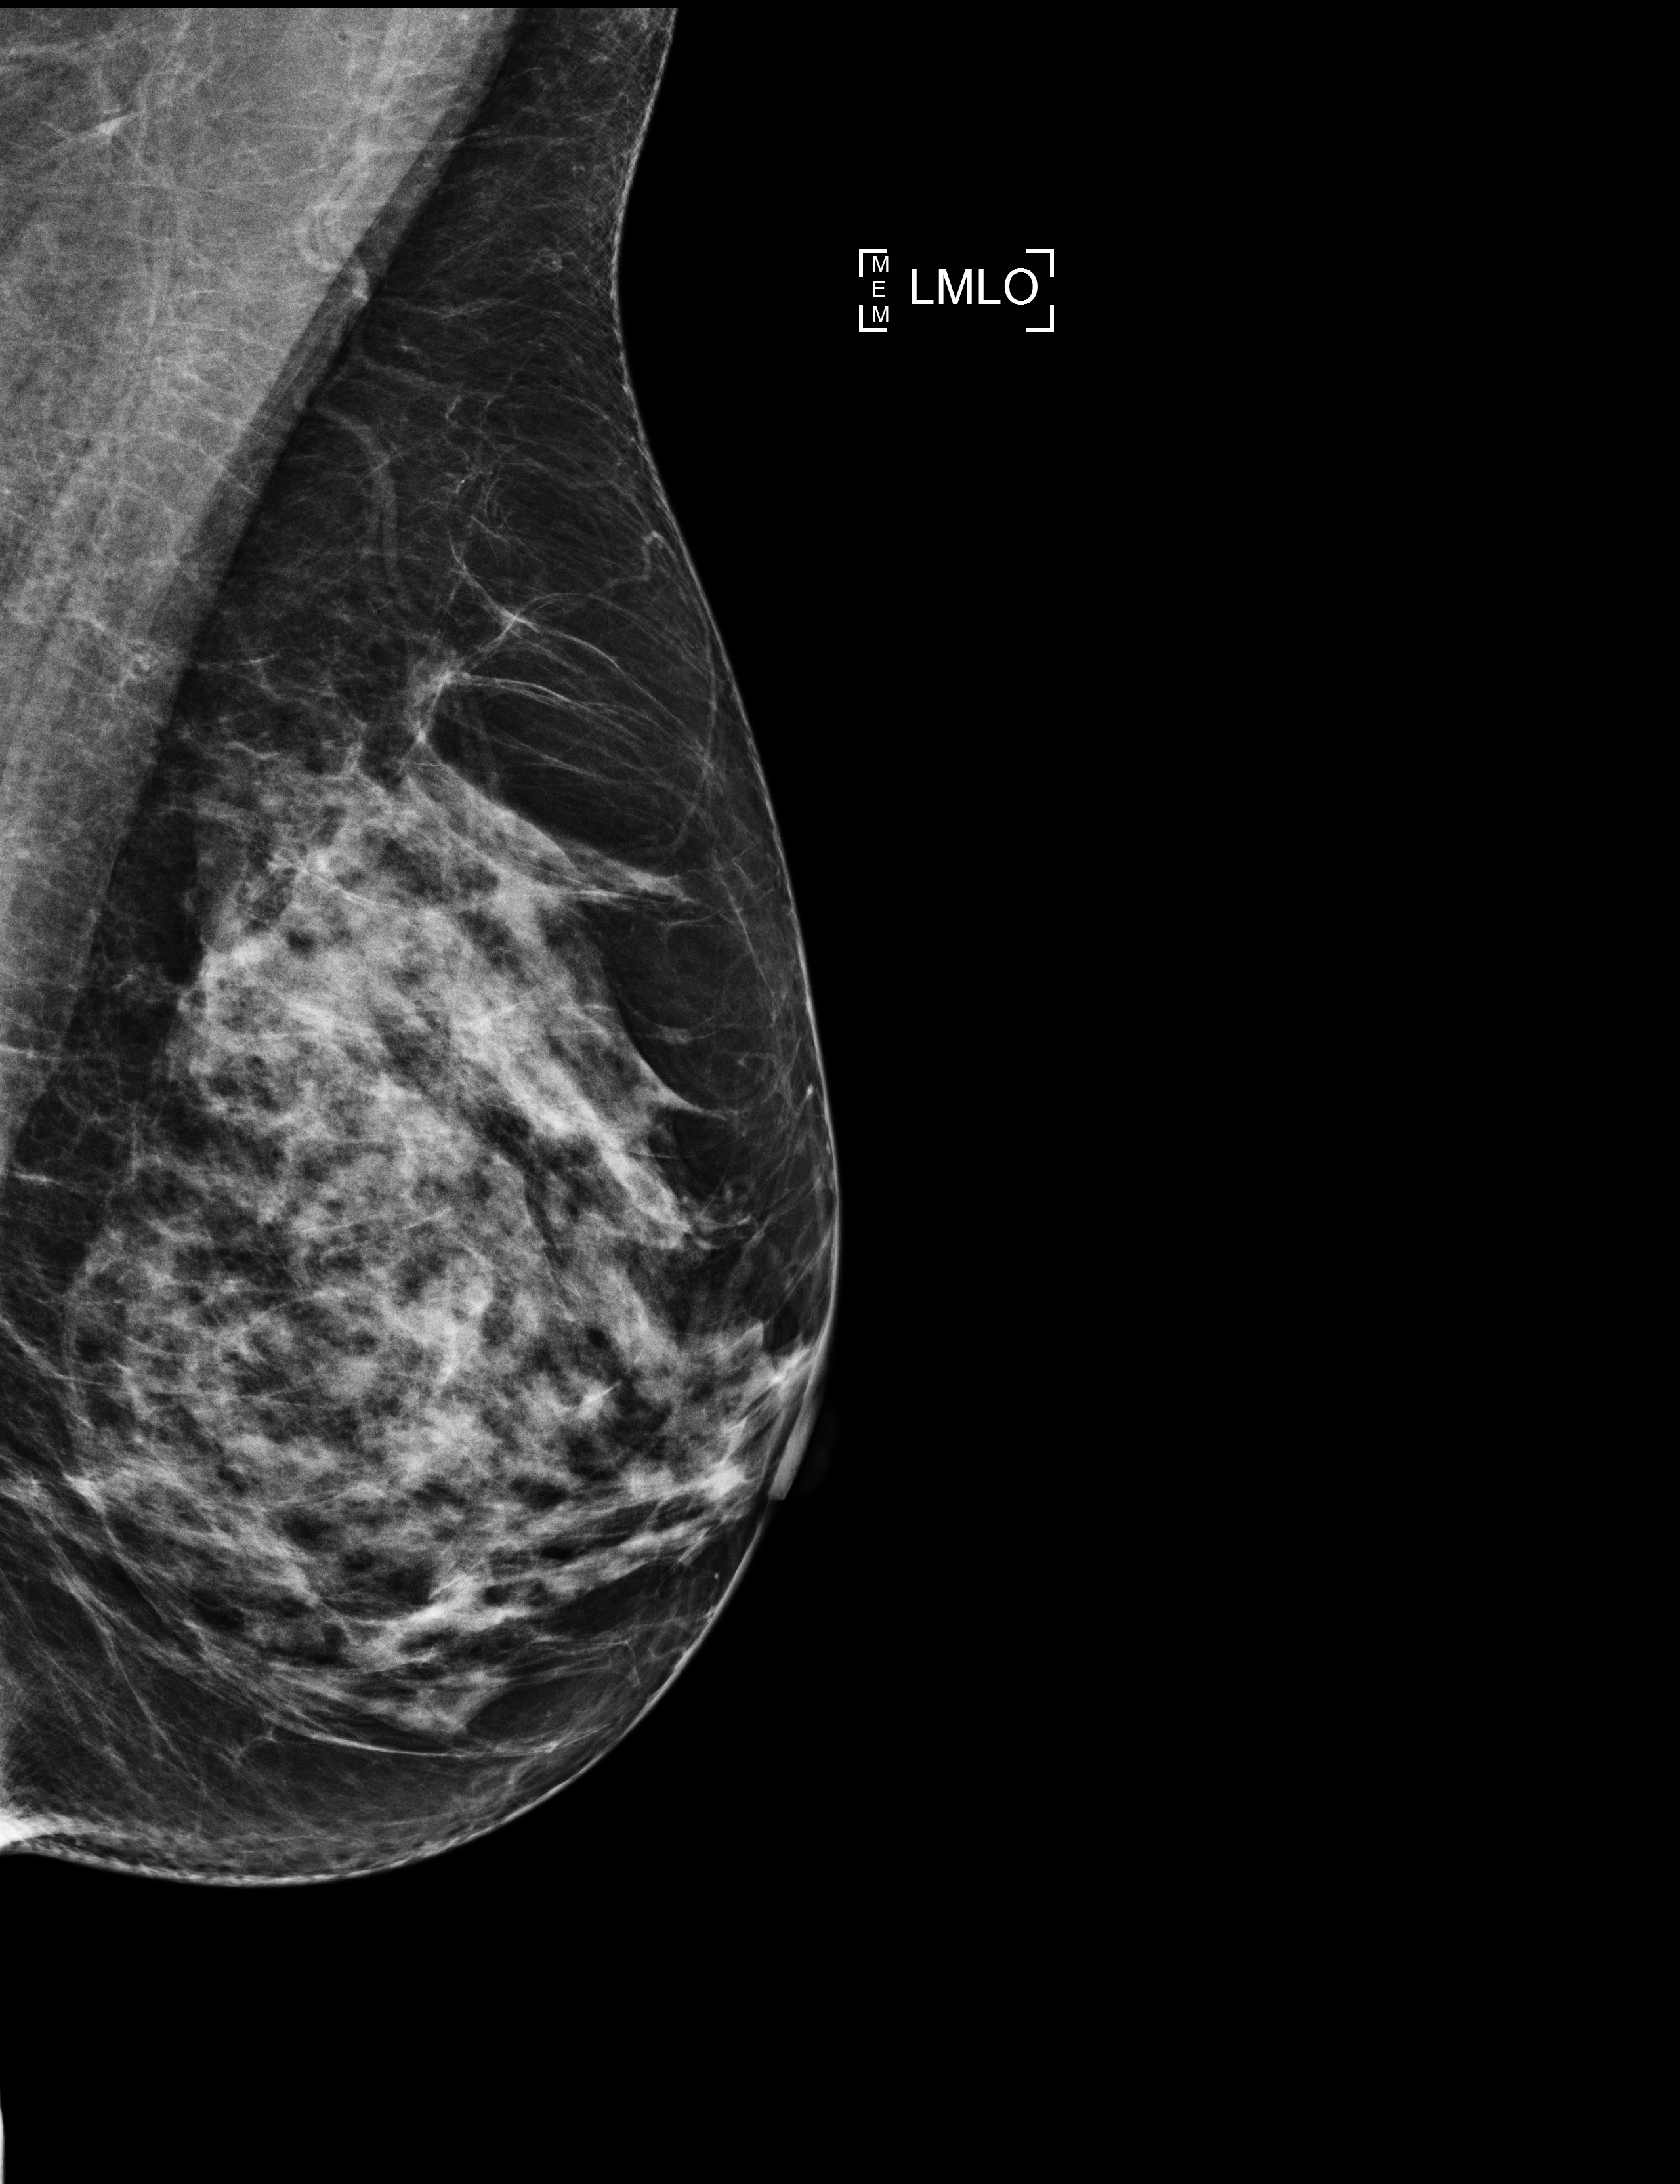
Full-field digital mammogram (FFDM); left breast; mediolateral oblique (MLO) view; annual screening mammography examination; compressed breast thickness 57 mm. Female patient, age 57 years.
Breast density at the screening exam (both breasts): heterogeneously dense (BI-RADS density category c). Final BI-RADS category for the screening round (tomosynthesis exam, both breasts): category 1. Recall: no recall after this screen.